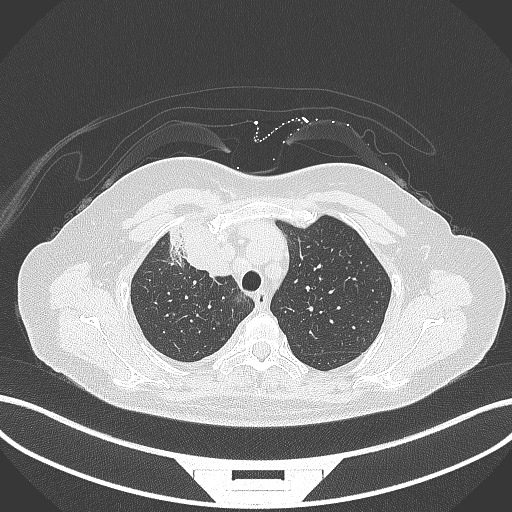
Chest CT, one axial slice; position 239 of 305 along the scan axis; 120 kVp; lung window (W 1500 / L -600 HU); 1 mm slice thickness; 512 × 512 image matrix, field of view 400 × 400 mm. Female patient, age 52 years. From the clinical record (not read from this slice): clinical TNM (as recorded): T3 N1 M1.
Annotated regions visible in this slice (rectangle marked by the reading radiologist):
- lung tumour (recorded histology: adenocarcinoma): box from (x=165, y=225) to (x=230, y=280) px